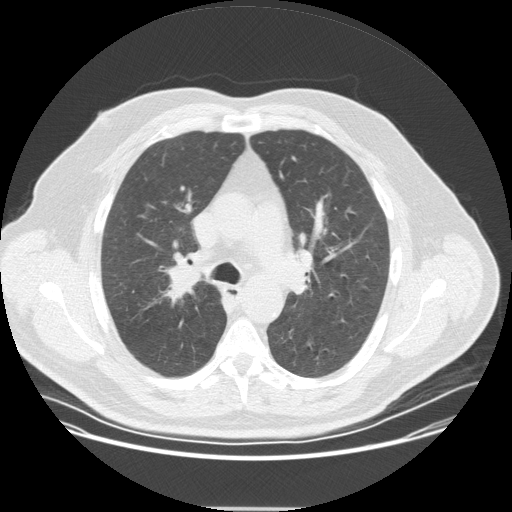
Low-dose screening chest CT, one axial slice; position 231 of 351 along the scan axis; 120 kVp; lung window (W 1500 / L -600 HU); 2.5 mm slice thickness; 512 × 512 image matrix, field of view 419 × 419 mm.
Outlined on this slice (expert manual segmentation):
- lesion 1 (tumor, upper lobe of right lung): bounding box (x1, y1, x2, y2) in pixels: (163, 267, 203, 304)